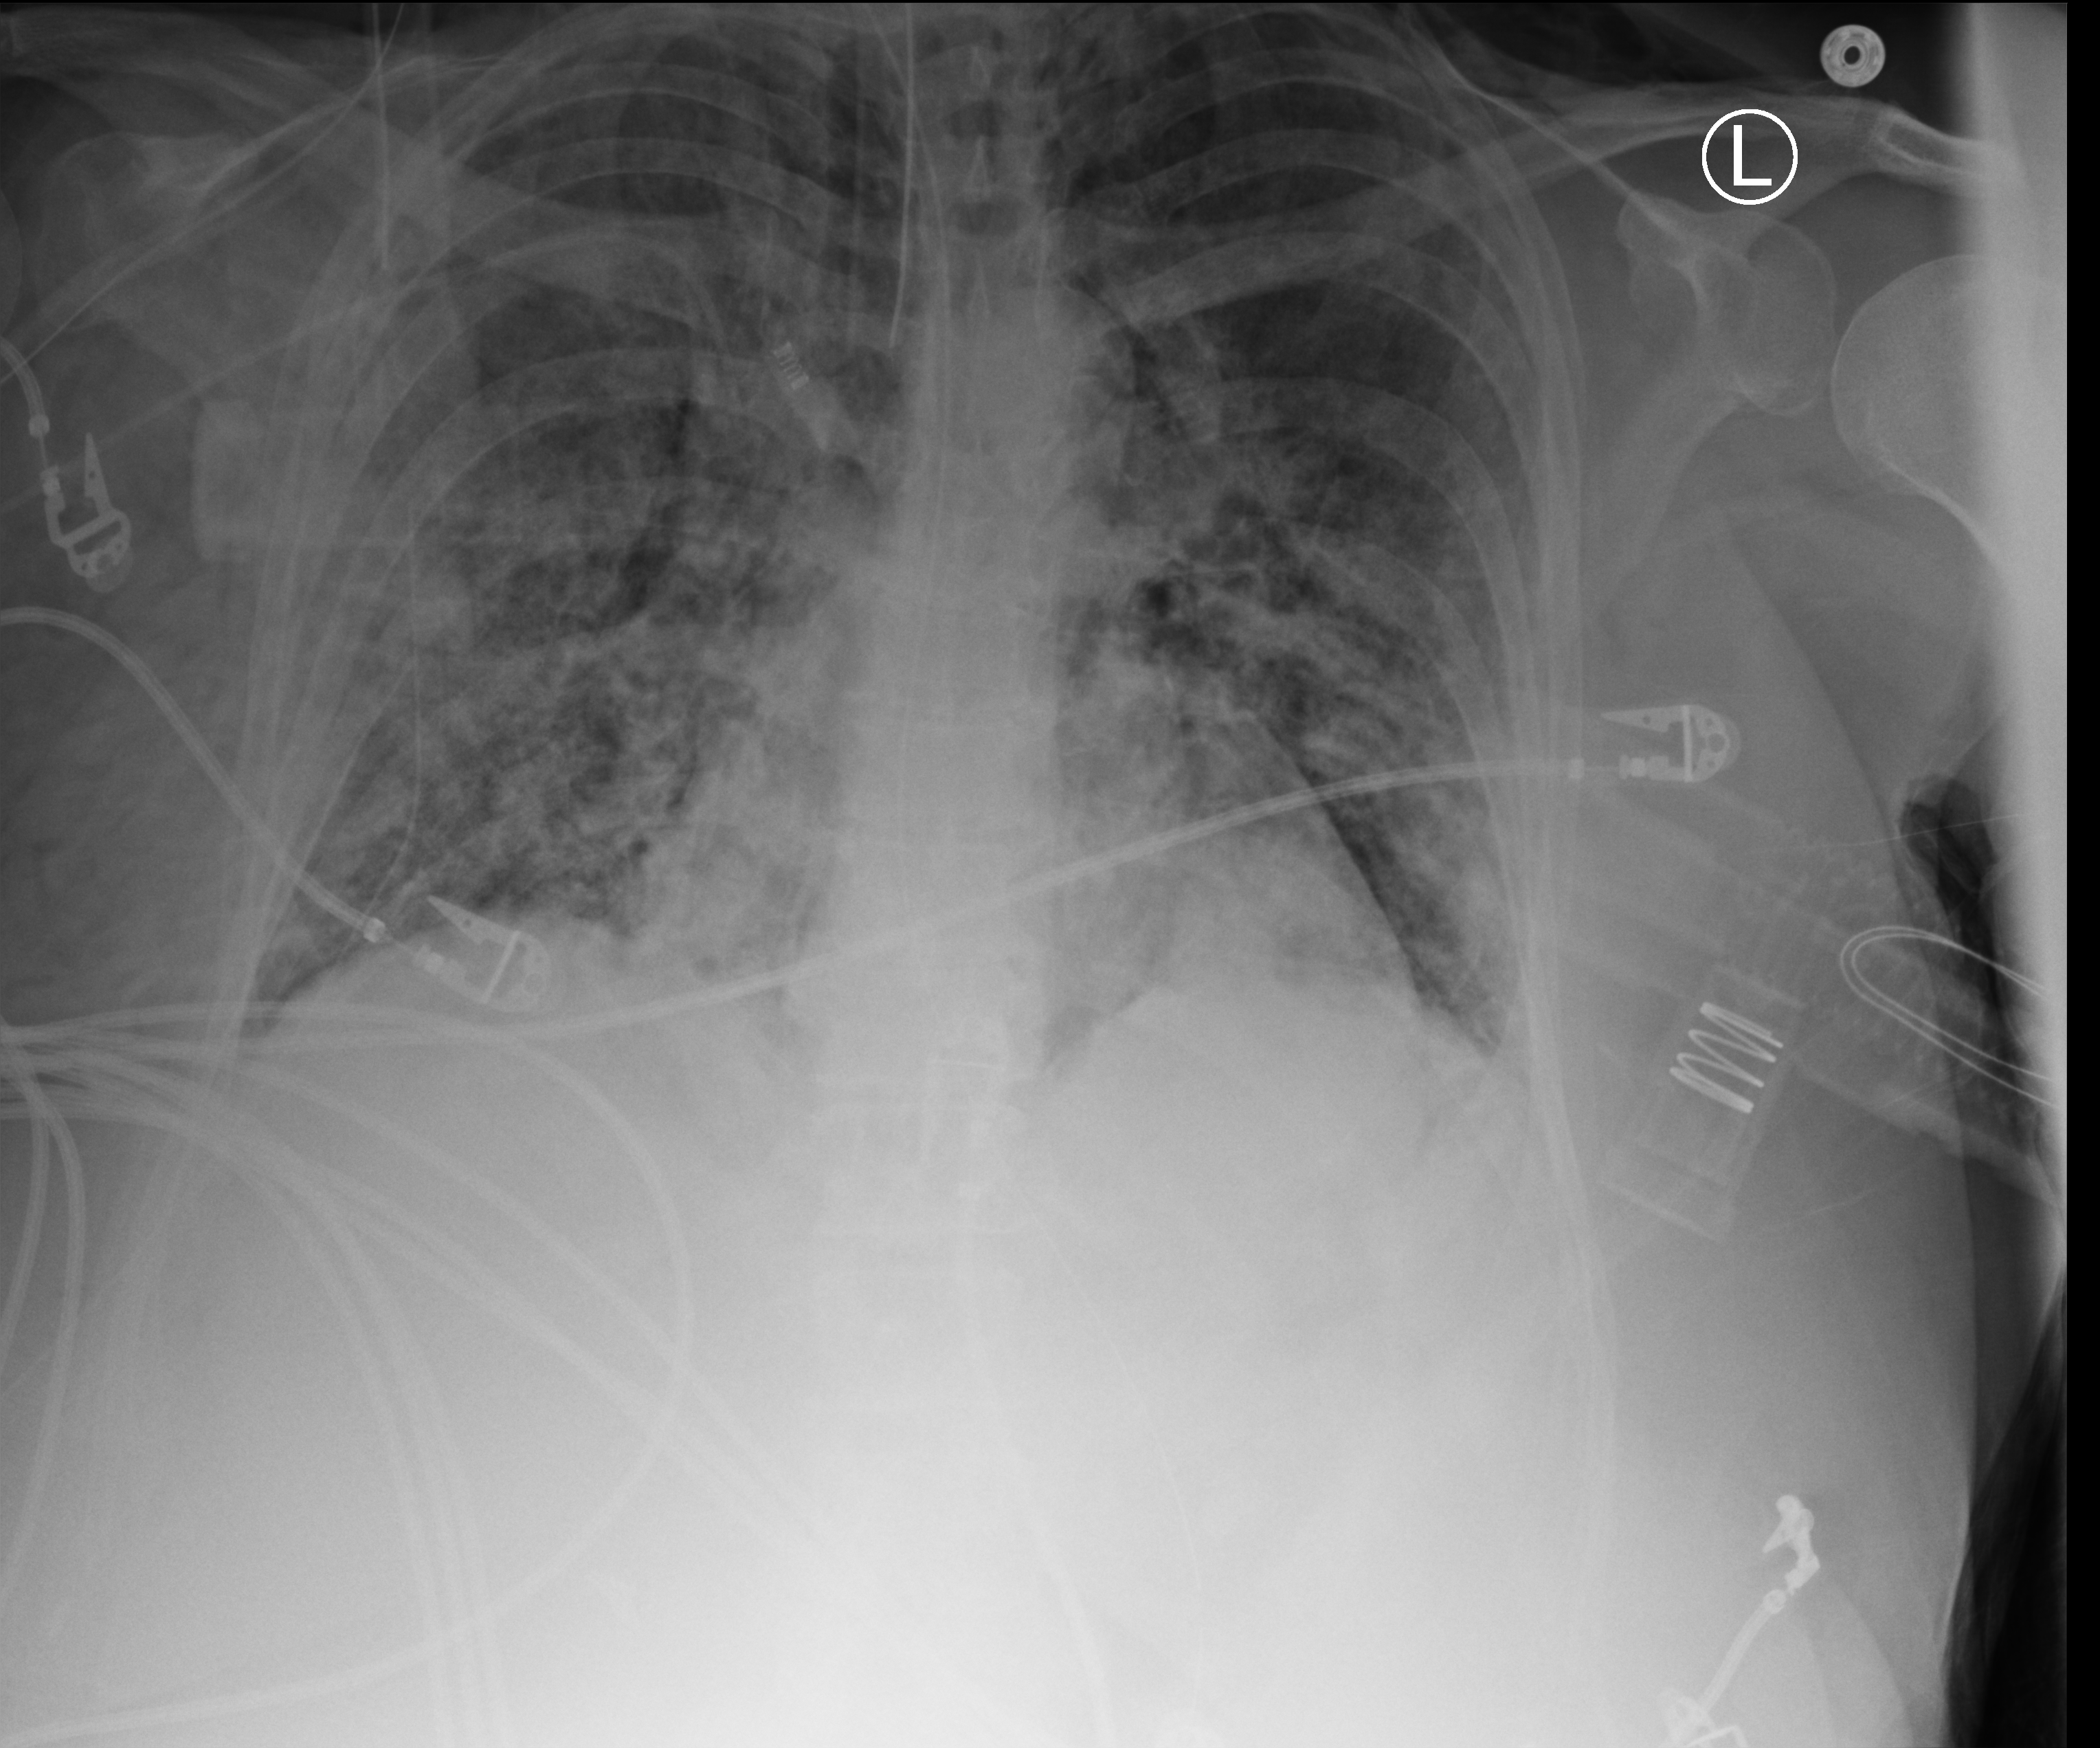
Portable chest radiograph. Patient hospitalised with COVID-19; female, aged 60–74 years.
Admission-level facts for this patient (not findings on this image; timing relative to this image not recorded):
- mechanically ventilated during this hospital stay: yes